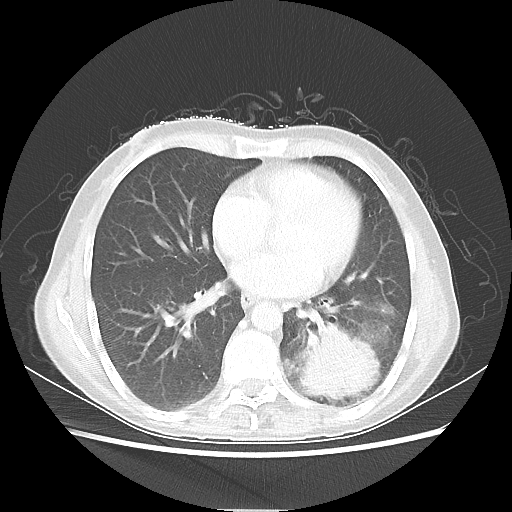
Chest CT, one axial slice. Position 24 of 56 along the scan axis. 80 kVp. Lung window (W 1500 / L -600 HU). 5 mm slice thickness. 512 × 512 image matrix. Female patient, age 53 years. Case-level facts recorded for this patient, not image findings: clinical TNM (as recorded): T3 N0 M0.
Outlined on this slice (rectangle marked by the reading radiologist):
- lung tumour (recorded histology: adenocarcinoma): bounding box (x1, y1, x2, y2) in pixels: (298, 326, 381, 399)